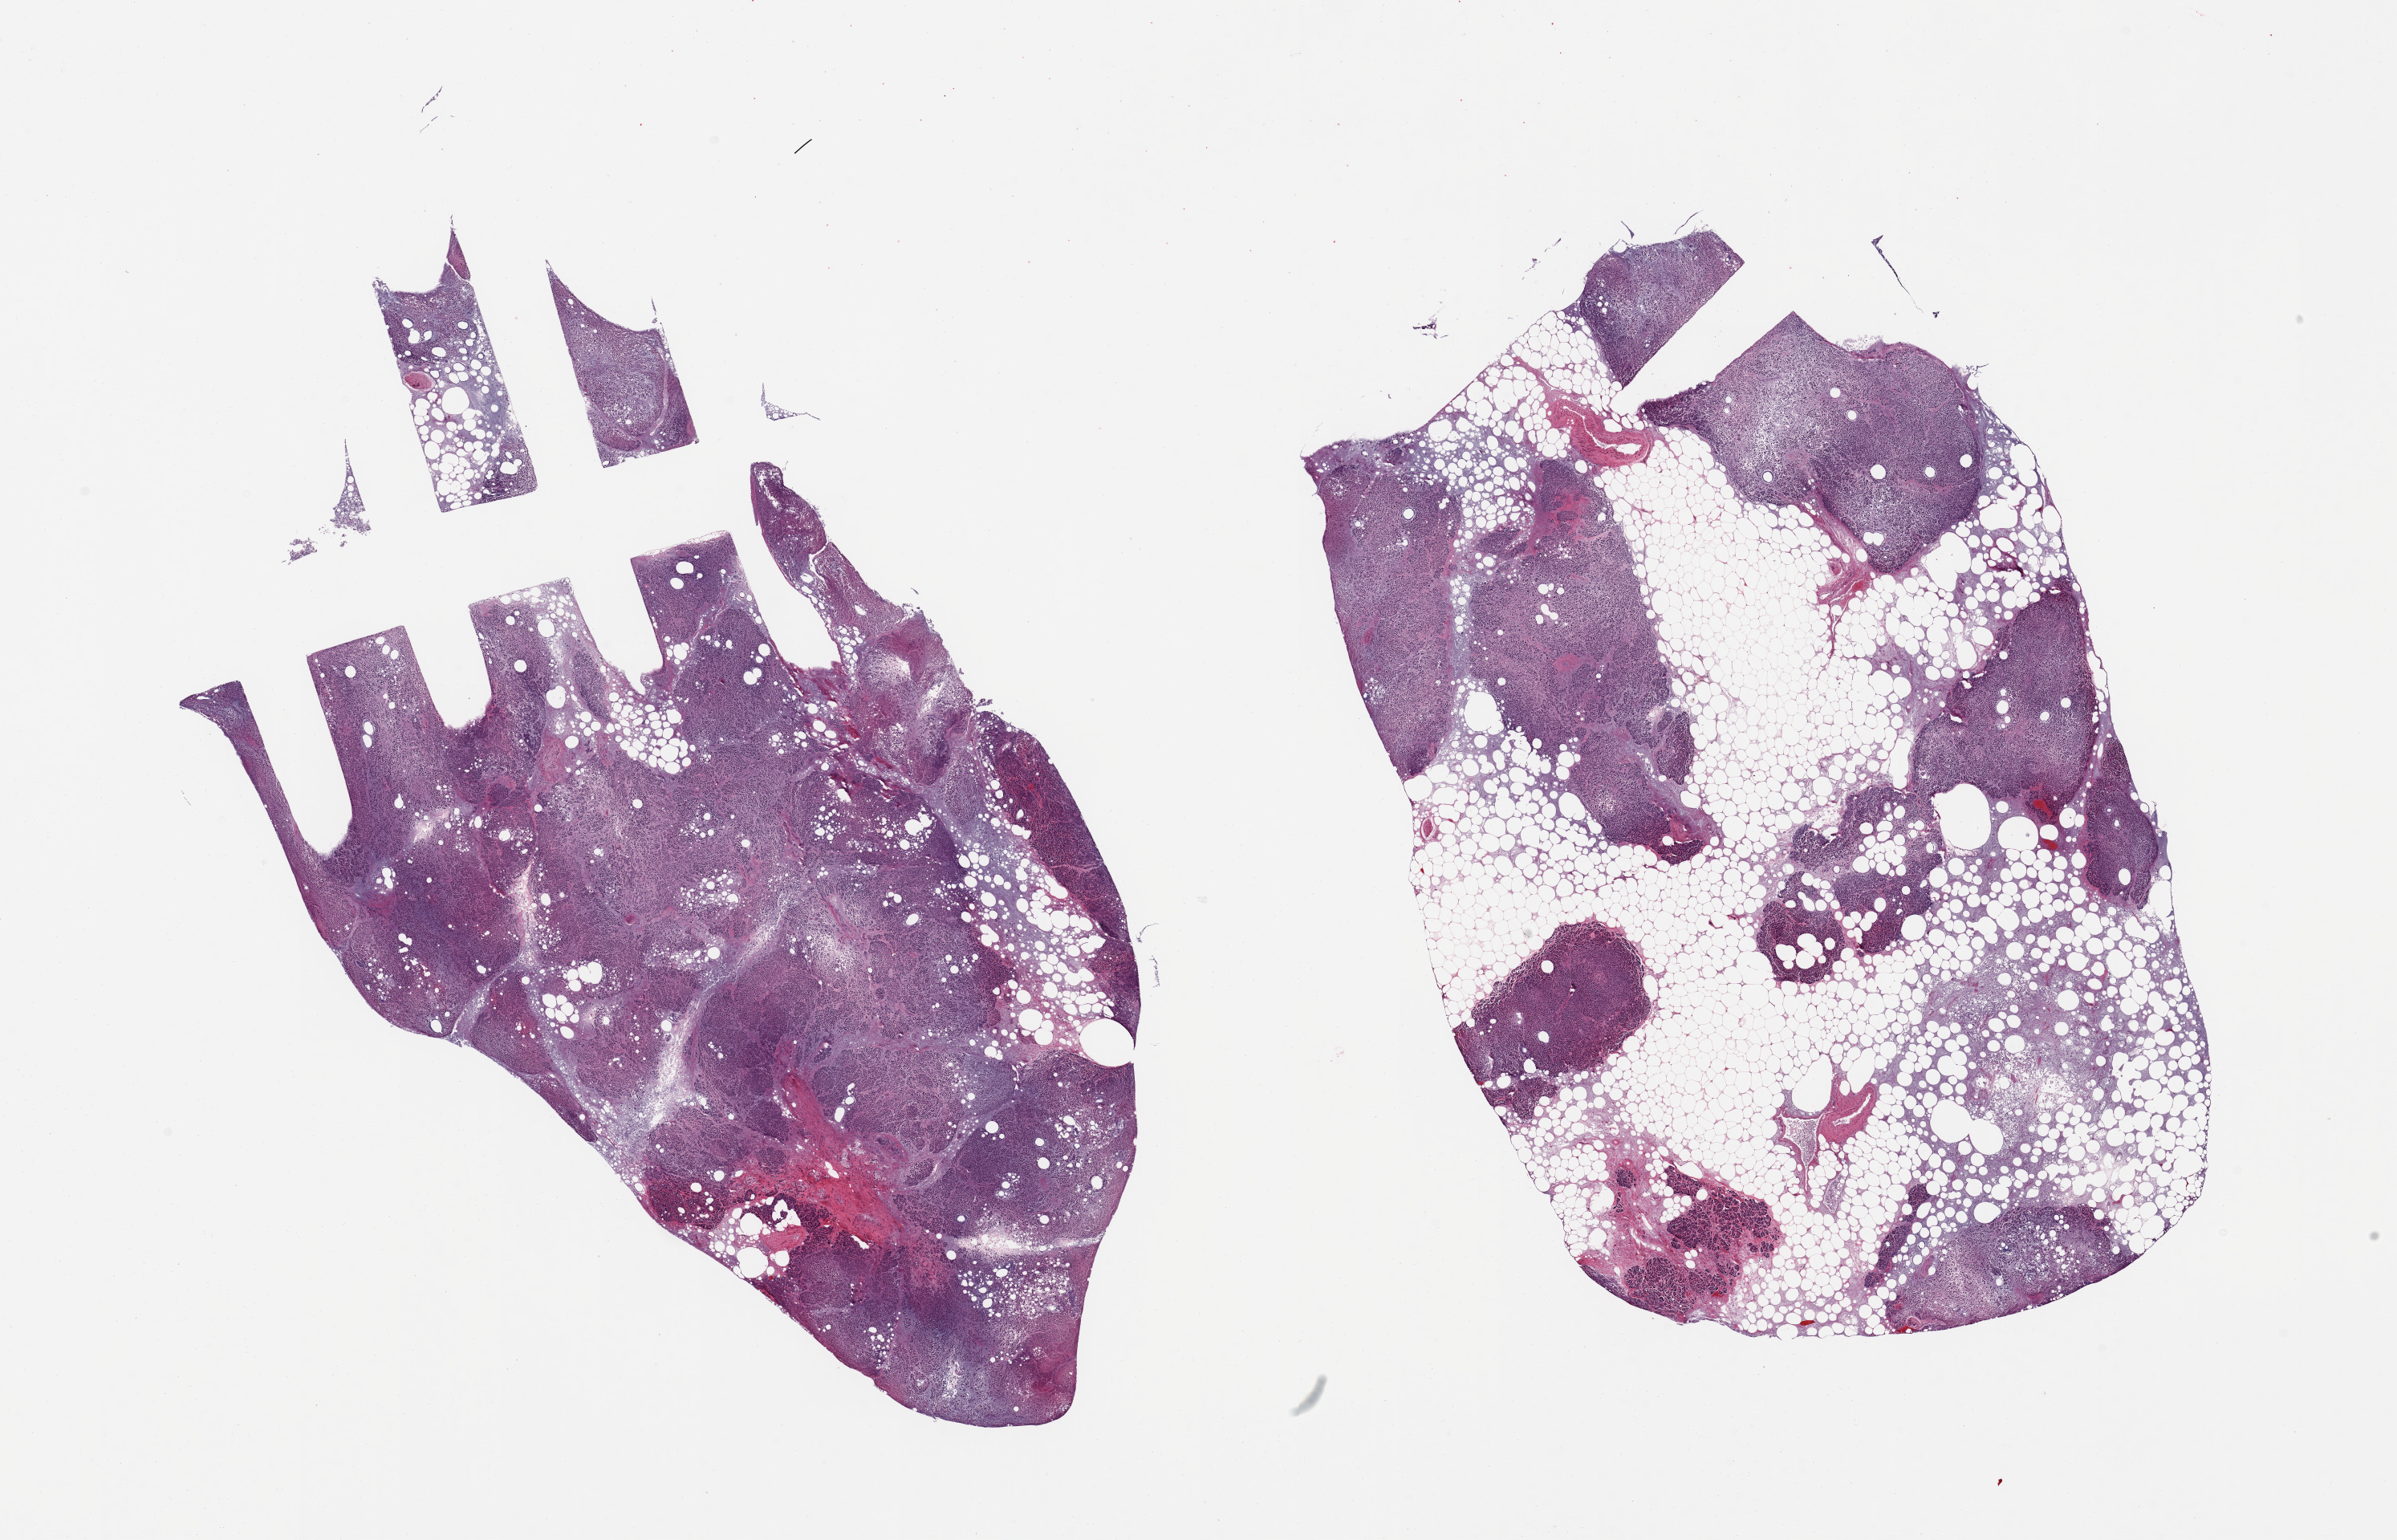
Digitized H&E-stained section, brightfield — low-resolution overview of the scanned area, about 23.6 x 15.2 mm (acquisition: 20x scan); PAXgene-fixed paraffin-embedded (PFPE) section; section of pancreas (target tissue); donor tissue sample. Donor: male.
* review note (as recorded): 2 pieces; markedly autolyzed, up to 60% internal/external fat